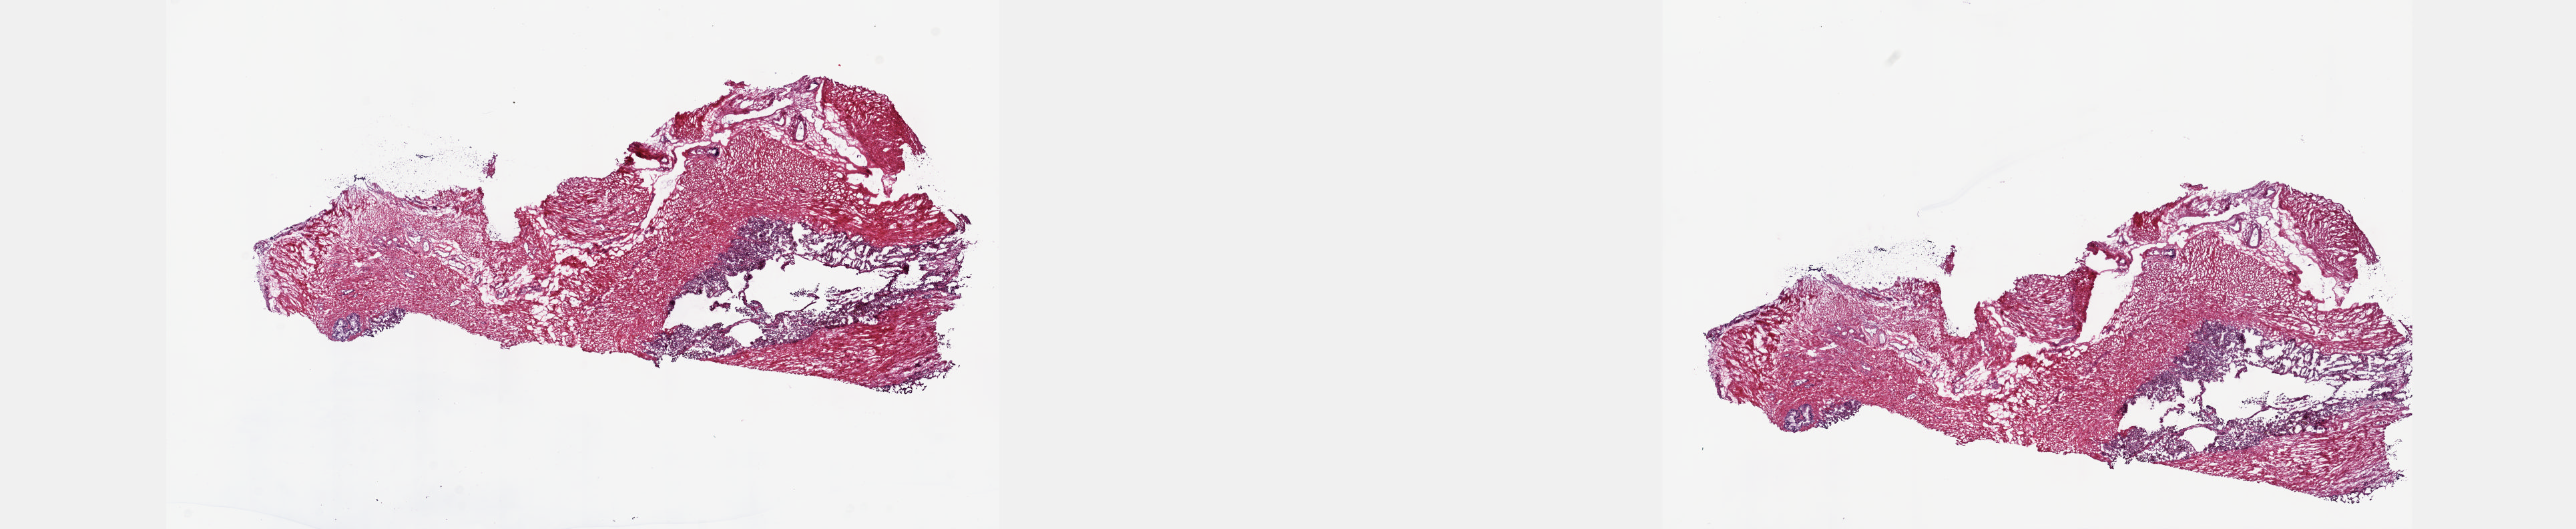
Whole-slide histology image, Hematoxylin and eosin (H&E) stained — low-resolution overview of the scanned area, about 31.1 x 6.4 mm (from a 20x scan). Frozen section. Prostate, solid tissue normal (non-tumour tissue) sample. Male, age 55 years at initial diagnosis. Composition of this section per pathologist review: tumour cells 0%, tumour nuclei 0%, normal cells 30%, stromal cells 70%, necrosis 0%. Infiltration values recorded for this section: lymphocyte infiltration 0%, monocyte infiltration 0%, neutrophil infiltration 0%.
• this section: solid tissue normal (non-tumour) sample from the same patient
• patient diagnosis: Adenocarcinoma, NOS (prostate gland)